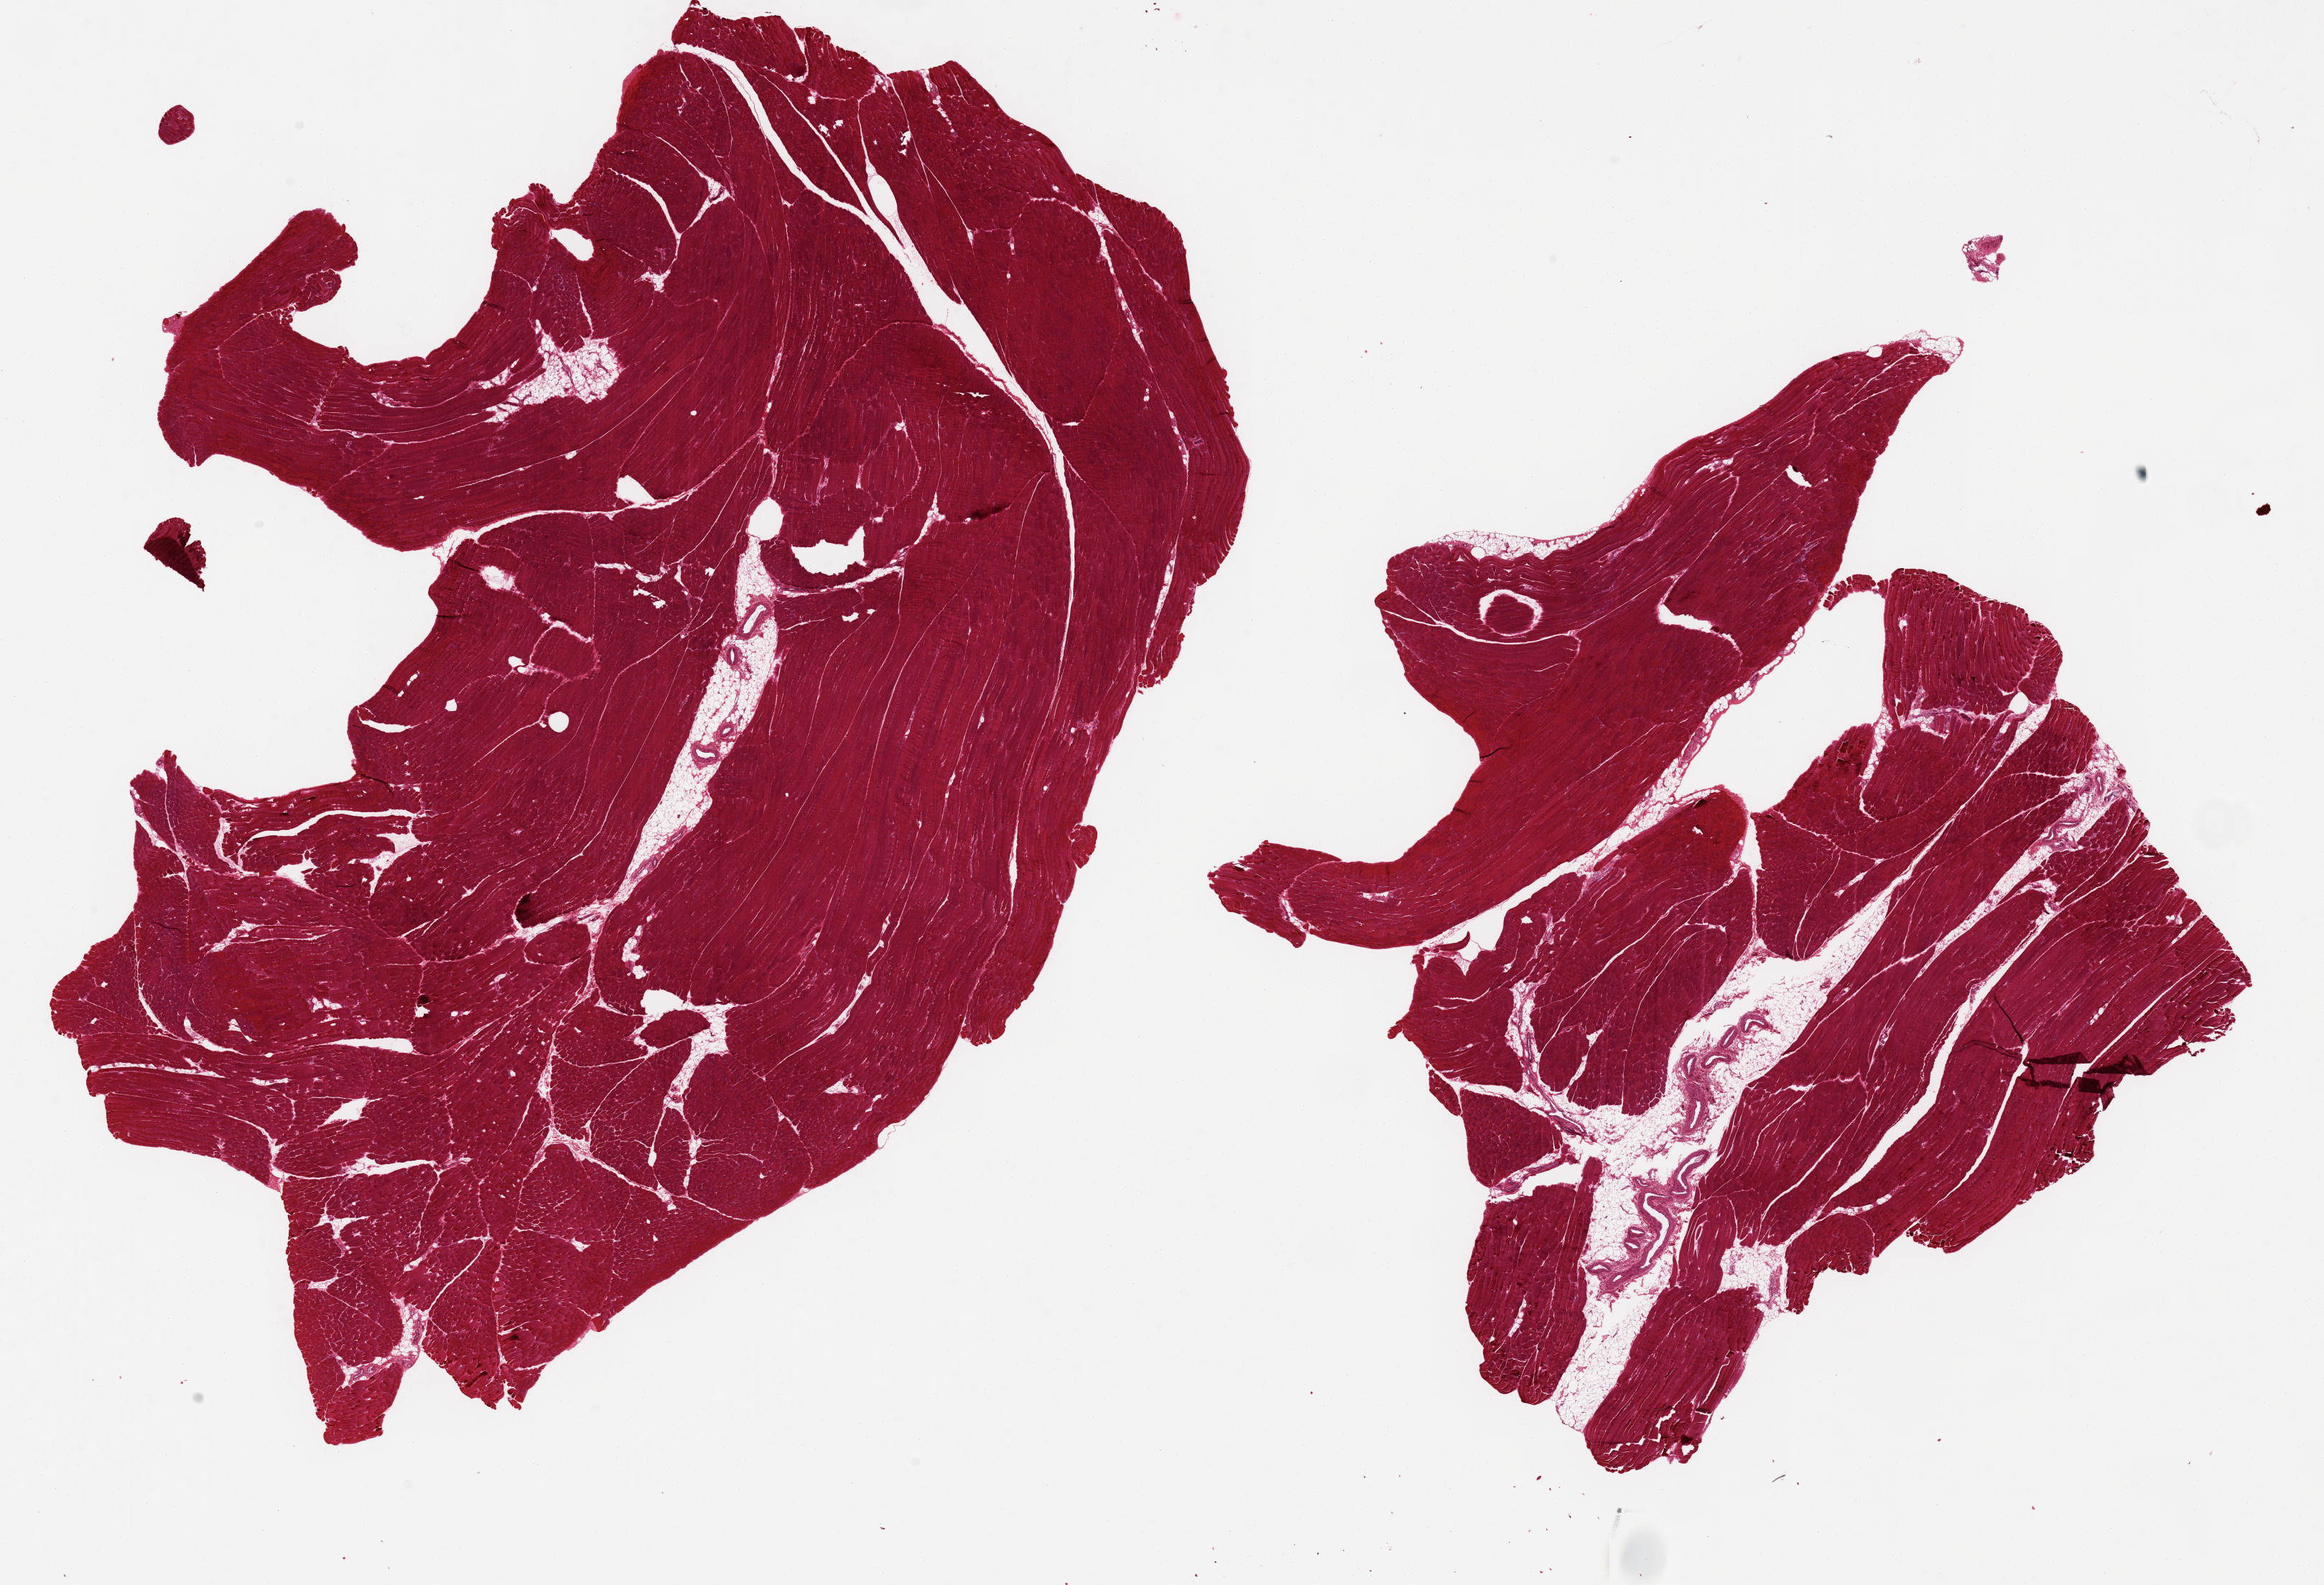
Whole-slide image, hematoxylin and eosin (H&E) stain, brightfield — a low-resolution overview of the entire scanned area, about 25.6 x 17.5 mm; PAXgene-fixed paraffin-embedded (PFPE) section; sampled site (target tissue): skeletal muscle; donor tissue sample. Donor sex: male.
Pathologist's review note for this sample: 2 pieces: 15x11 & 9.5x9.5 mm; ~5% internal fat.